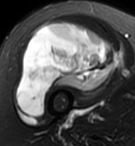
MRI of an extremity soft-tissue mass, one axial slice; slice 59 of 95 in the series (ordered by position); T2-weighted fat-saturated; MR volume resampled by the dataset authors to the PET/CT grid (not the native acquisition matrix); 3.27 mm slice thickness; 135 × 146 image matrix, field of view 132 × 143 mm. Female patient. Case-level facts recorded for this patient, not image findings: histological type: pleiomorphic undifferentiated sarcoma; grade: high; site of the primary tumour: right quadricep.
Structures marked on this image (expert contour drawn on MRI and transferred to this co-registered scan by the dataset authors):
- gross tumour volume including surrounding oedema: bounding box [x1, y1, x2, y2] px = [16, 20, 118, 117]
- gross tumour volume (mass): [16, 20, 118, 117]